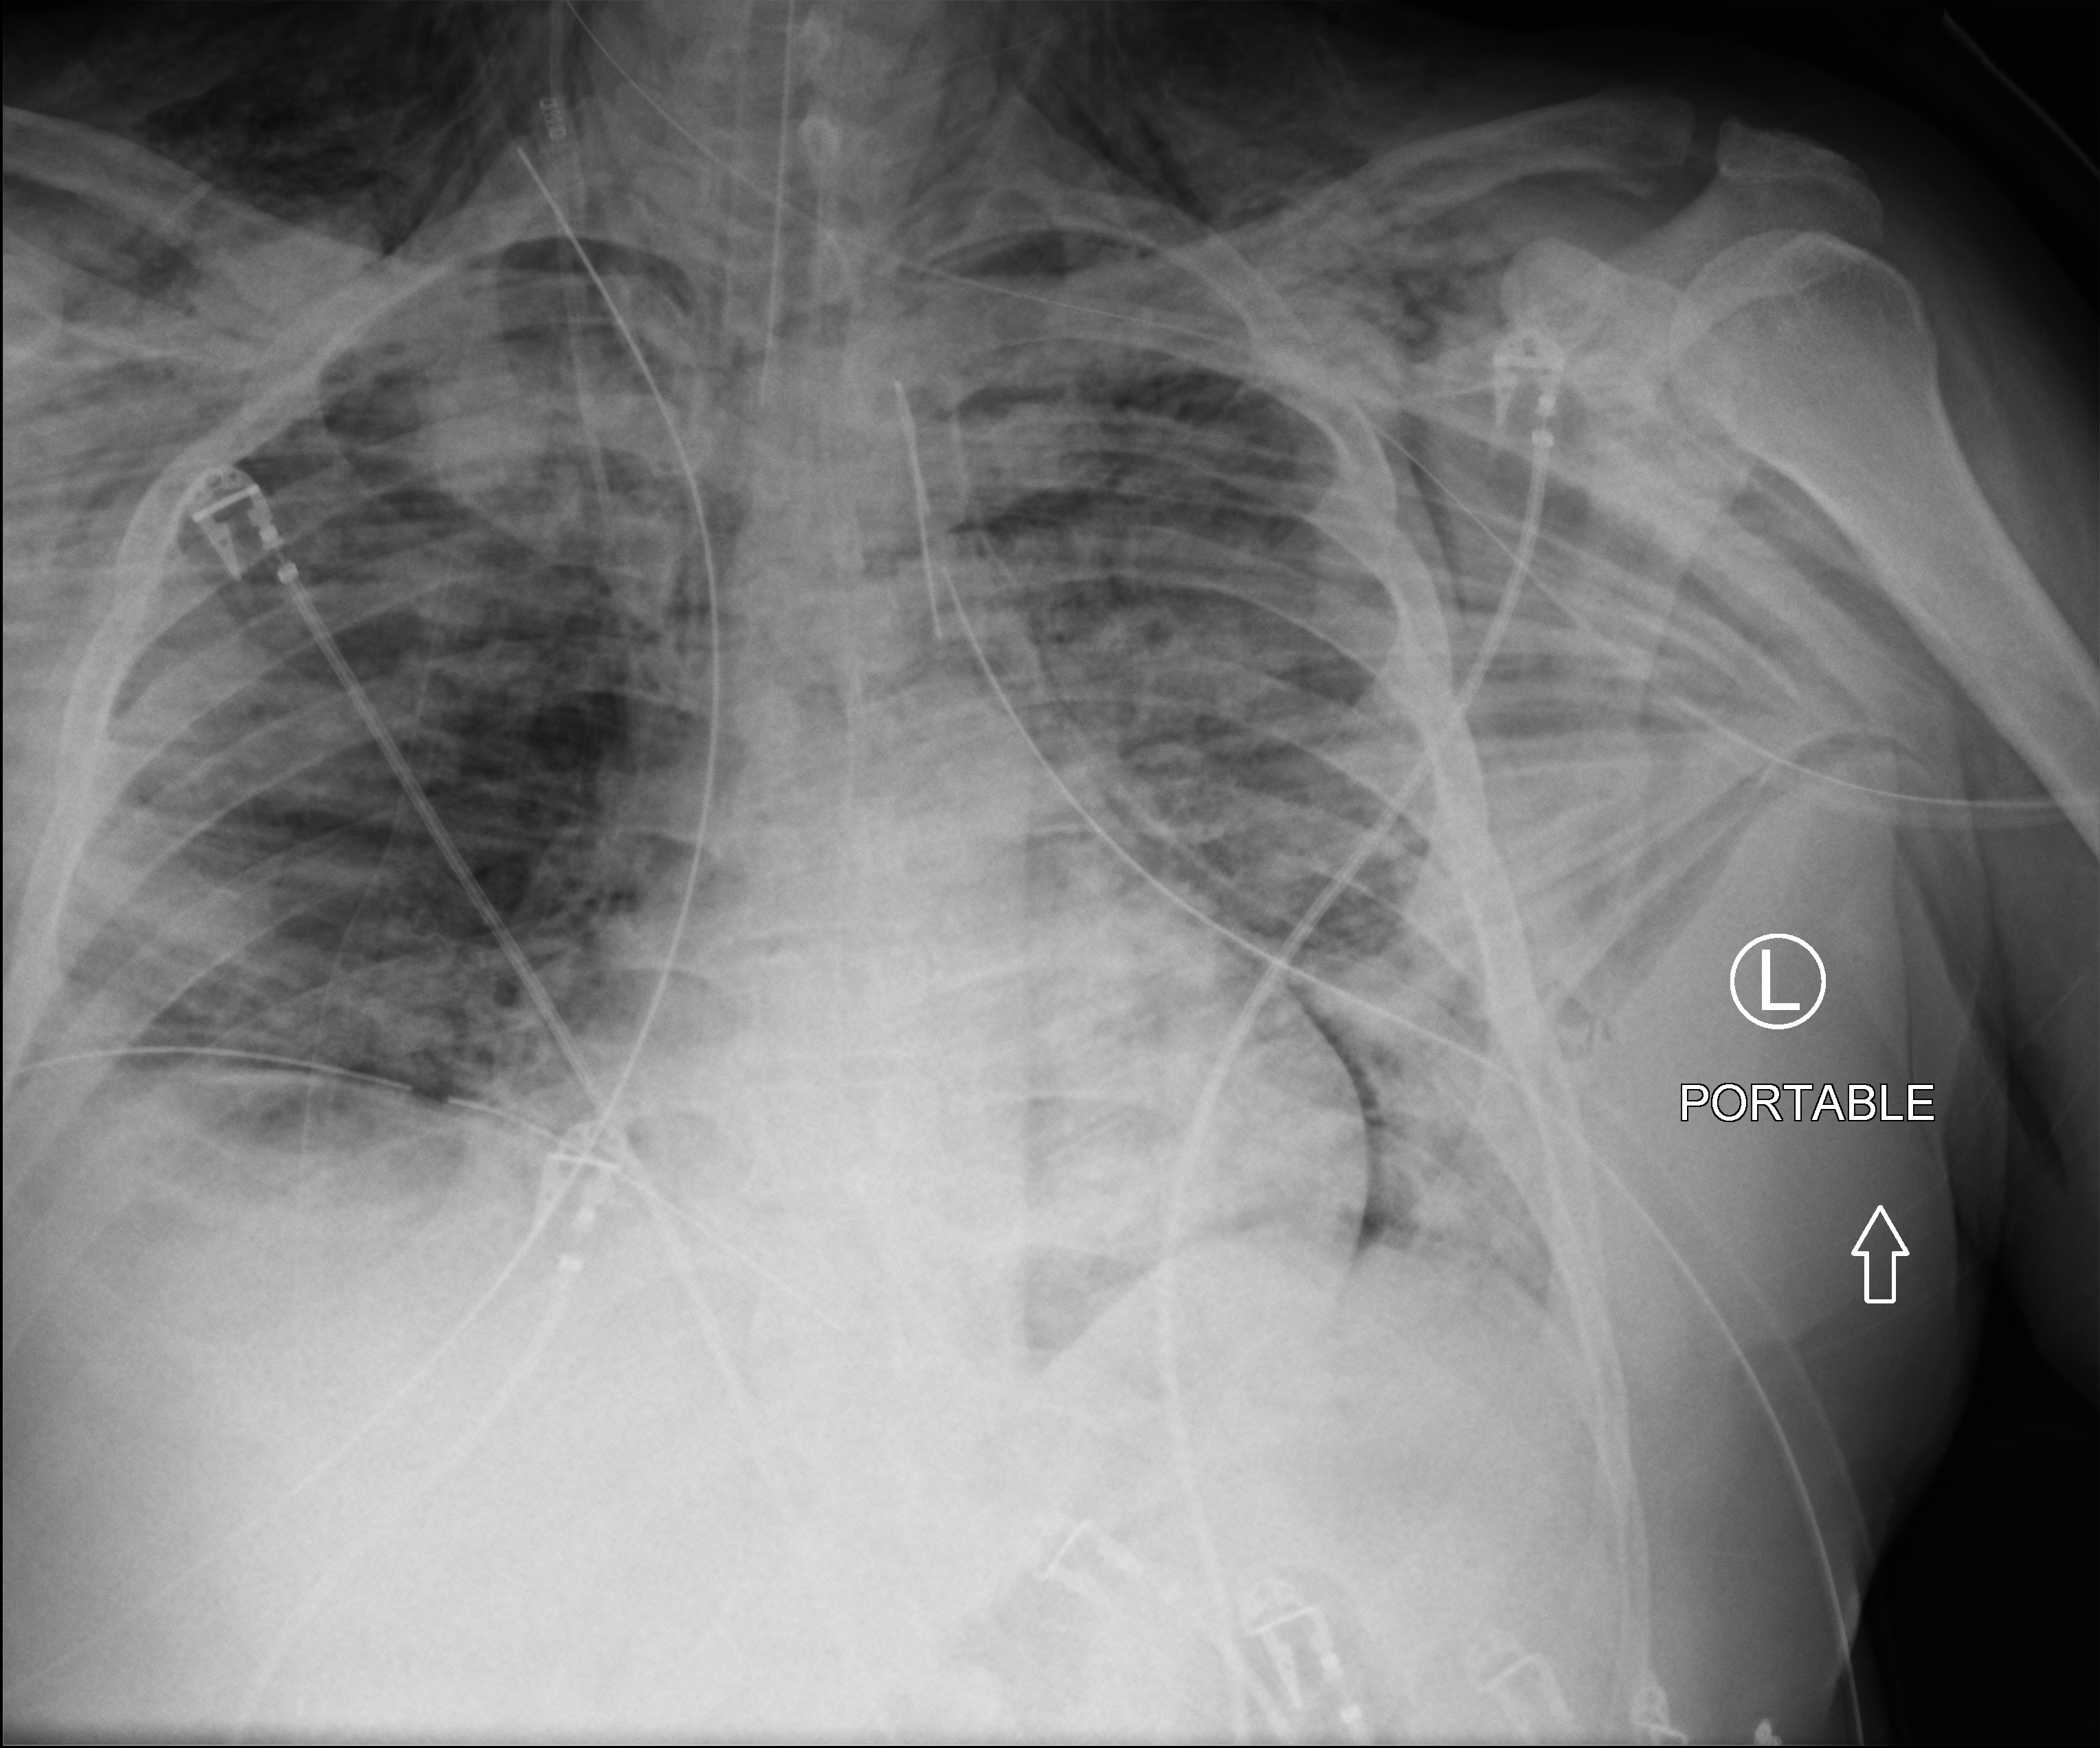
Chest X-ray (portable). Male patient hospitalised with COVID-19, age 18–59 years.
From the hospital-stay record, not from the radiograph (when in the stay this image was taken is not recorded): admitted to intensive care during this hospital stay: yes; mechanically ventilated during this hospital stay: yes.